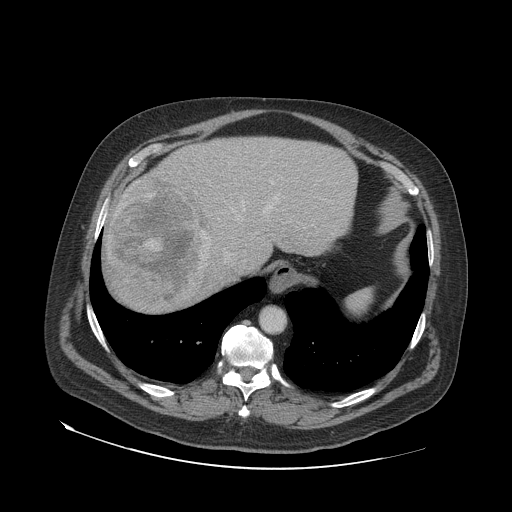
Contrast-enhanced abdominal CT (liver protocol), one axial slice. Reconstruction kernel STANDARD. 140 kVp. Soft-tissue window (W 400 / L 40 HU). 2.5 mm slice thickness. 512 × 512 image matrix. From the clinical record (not read from this slice): diagnosis: hepatocellular carcinoma (patient treated with transarterial chemoembolisation; whether this scan precedes or follows treatment is not stated here); TNM stage (as recorded): Stage-IVA; Child-Pugh class: A; tumour nodularity: multinodular.
Annotated regions visible in this slice (semi-automatically segmented with operator editing):
- abdominal aorta: bounding box <261,307,285,332> (left, top, right, bottom; pixels)
- liver parenchyma outside the tumour (the mass and vessels are separate outlines, so this box may not span the whole liver): <104,136,356,312>
- mass: <107,177,210,308>
- liver vessels: <242,182,279,212>